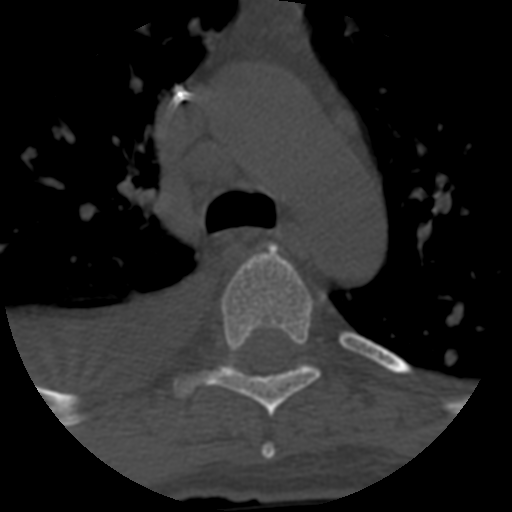
CT including the spine, one axial slice; position 454 of 708 along the scan axis; reconstruction kernel STANDARD; one of 3 acquisitions stored at this slice position; bone window (W 1800 / L 400 HU); 1.25 mm slice thickness; 512 × 512 image matrix, field of view 160 × 160 mm. Patient age 55 years. Case-level facts recorded for this patient, not image findings: primary cancer: colon; vertebrae with lytic lesions (as recorded): T12, L1, L5.
Annotated regions visible in this slice (semi-automatically segmented with operator editing):
- T4 vertebra: bounding box <261,445,276,459> (left, top, right, bottom; pixels)
- T5 vertebra: <177,245,320,417>